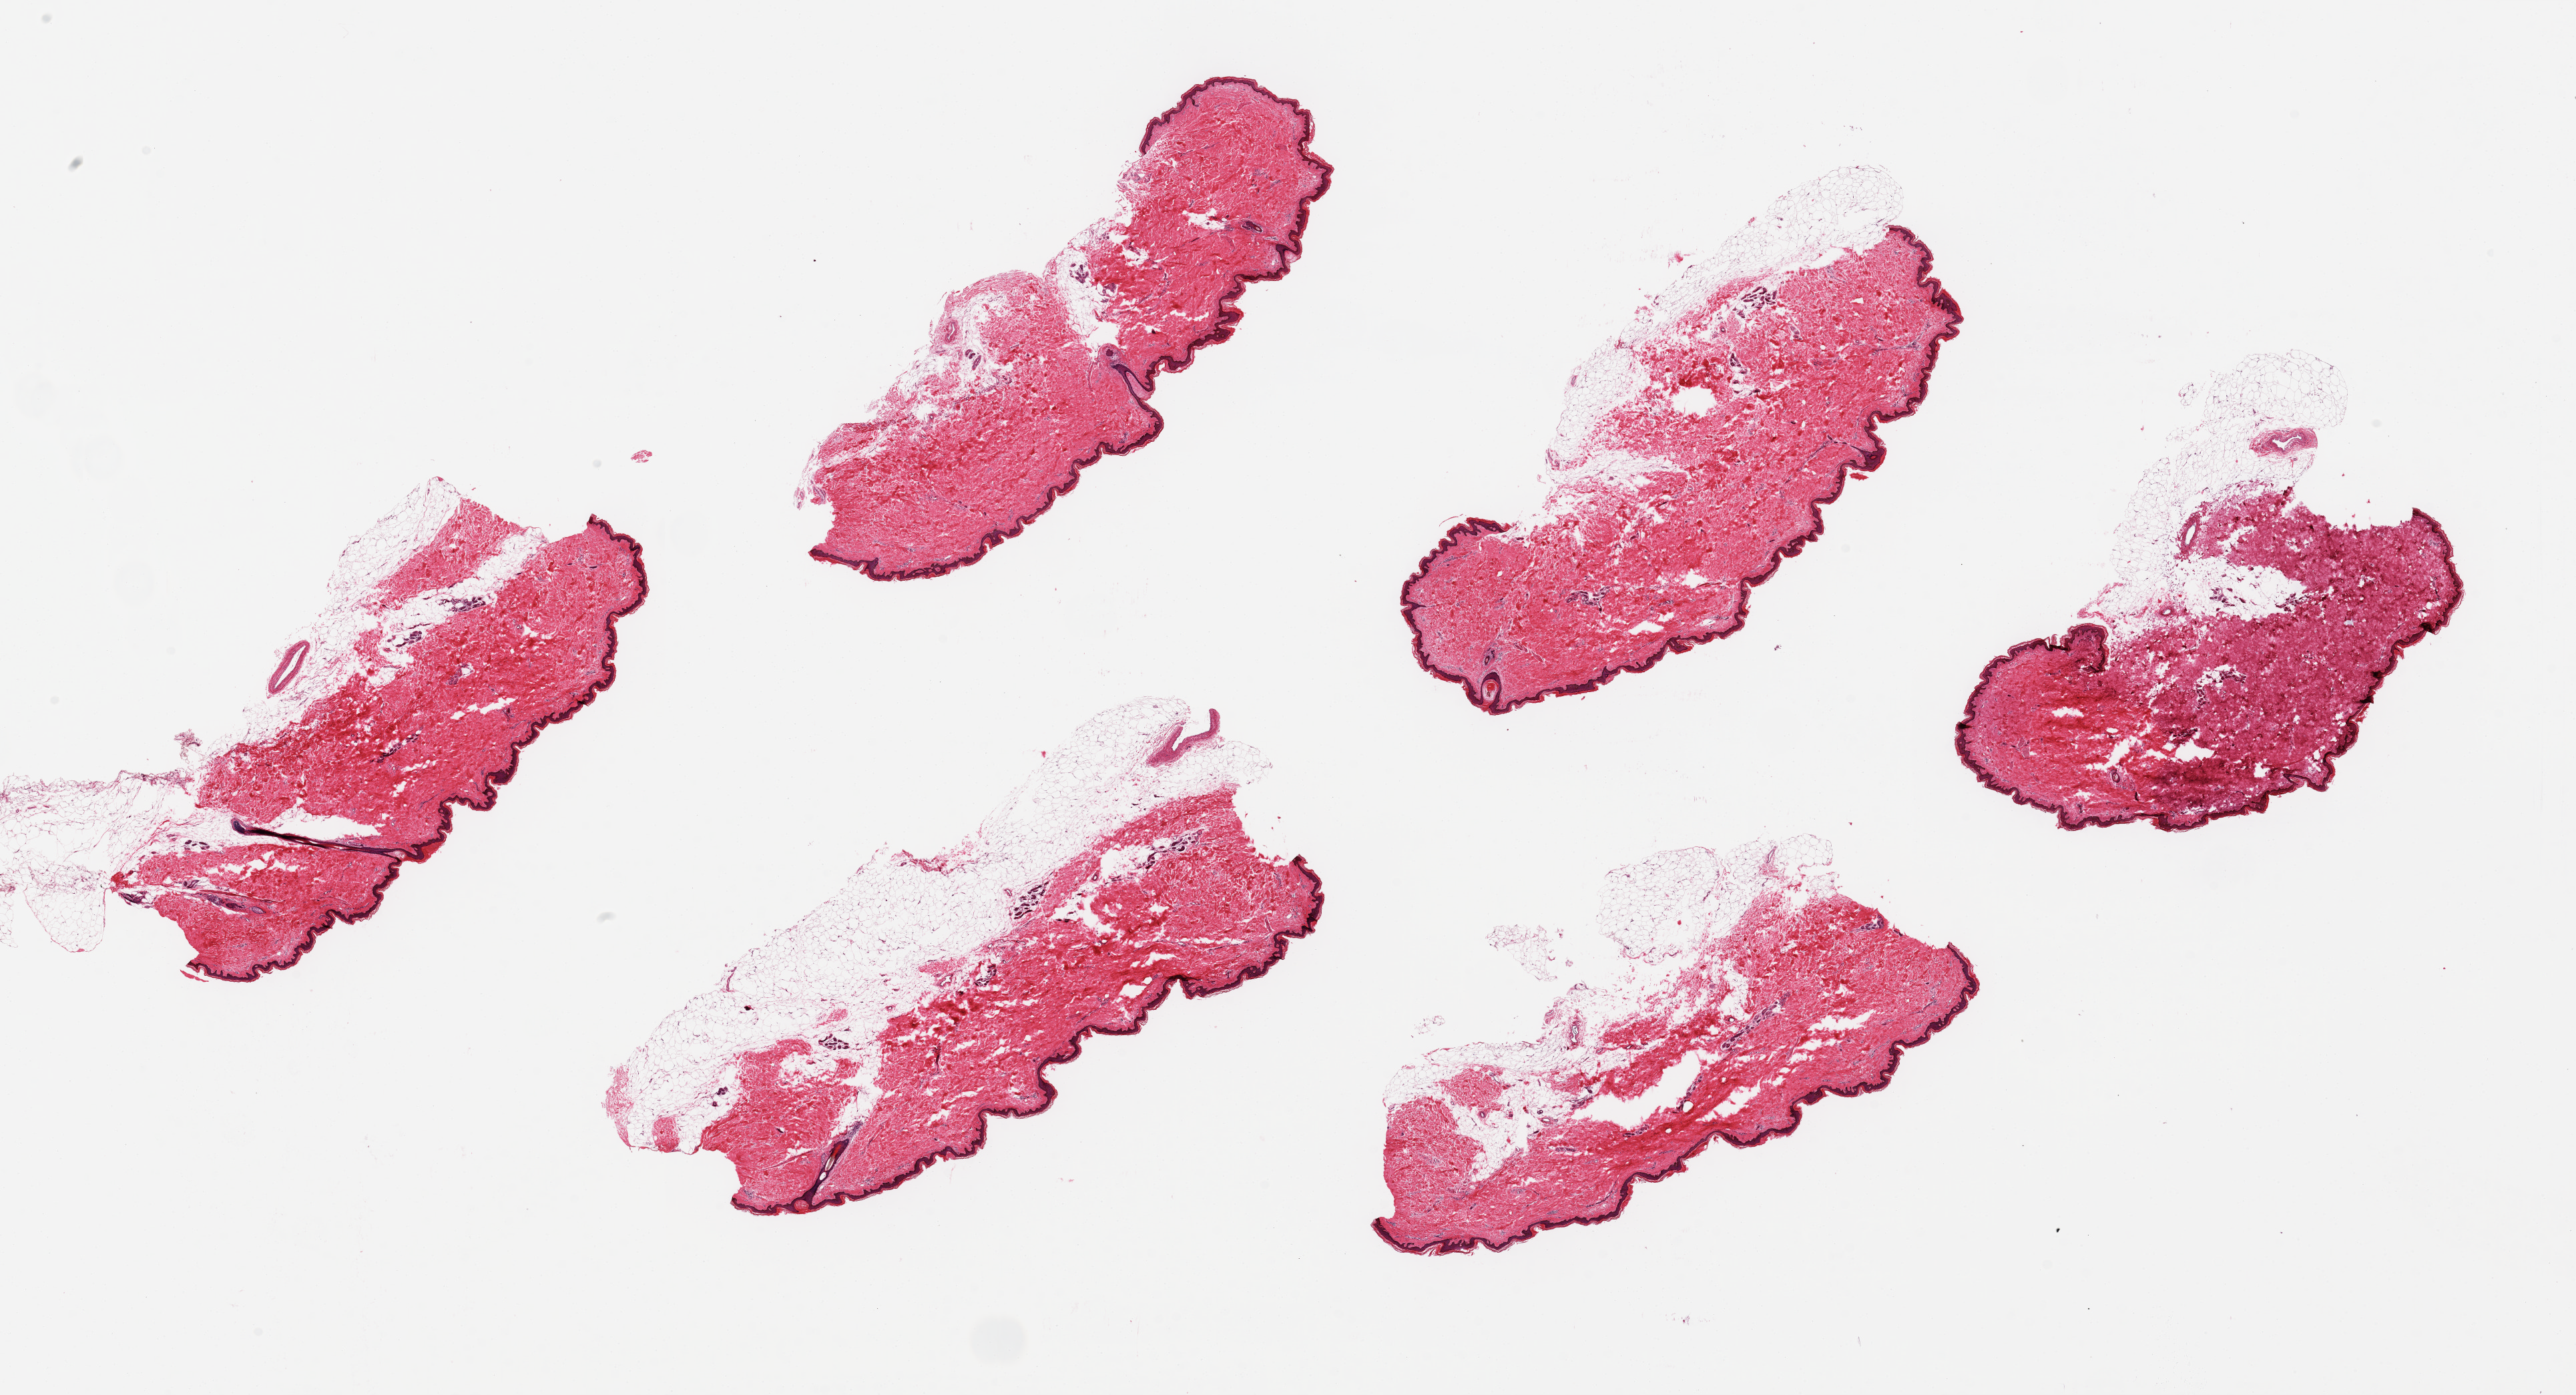
Whole-slide image, haematoxylin and eosin stain, whole scanned area (about 30.5 x 16.5 mm, acquisition: 20x scan) shown as a low-resolution overview. PAXgene-fixed paraffin-embedded (PFPE) section. Section of skin of lower leg (target tissue). Donor tissue sample. Donor sex: female.
* pathologist's review note for this sample: 6 pieces up to 8x3.4 mm